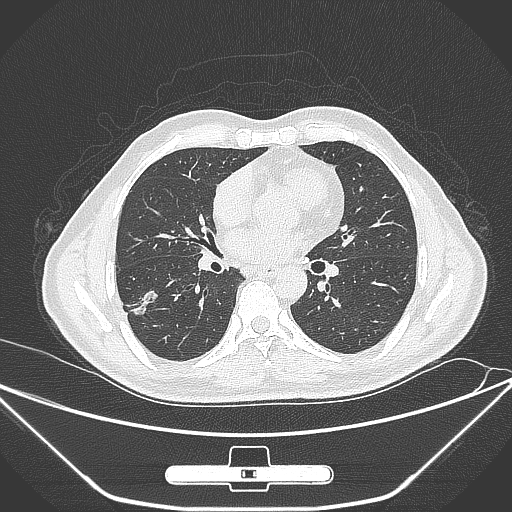
Chest CT, one axial slice. Slice 142 of 310 in the series (ordered by position). 120 kVp. Lung window (W 1500 / L -600 HU). 1 mm slice thickness. 512 × 512 image matrix, field of view 398 × 398 mm. Male patient, age 71 years. From the clinical record (not read from this slice): clinical TNM (as recorded): T1c N0 M0.
Annotated regions visible in this slice (bounding box drawn by a radiologist):
- lung tumour (recorded histology: adenocarcinoma): bounding box [x1, y1, x2, y2] px = [131, 283, 160, 318]